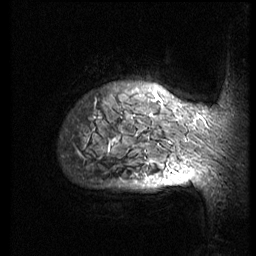
Breast MRI (dynamic contrast-enhanced), one sagittal slice. Slice 65 of 74 in the series (ordered by position). 3 images stored at this slice position (order not interpretable as contrast timing). 1.5 T. TE 4.2 ms, TR 8.9 ms. 2.5 mm slice thickness. 256 × 256 image matrix, field of view 200 × 200 mm. Patient: female, 57 years. Case-level facts recorded for this patient, not image findings: setting: breast cancer imaged before/during neoadjuvant chemotherapy; receptor status: HER2-positive.
Outlined on this slice (semi-automatic segmentation, software-assisted and operator-edited):
- analysis volume of interest (the breast-tissue region the enhancement analysis was run in; not a lesion): box from (x=60, y=67) to (x=247, y=173) px
- tumour enhancement mask (voxels above the 140 % enhancement threshold inside the analysis volume of interest): (x=109, y=94)–(x=188, y=173)